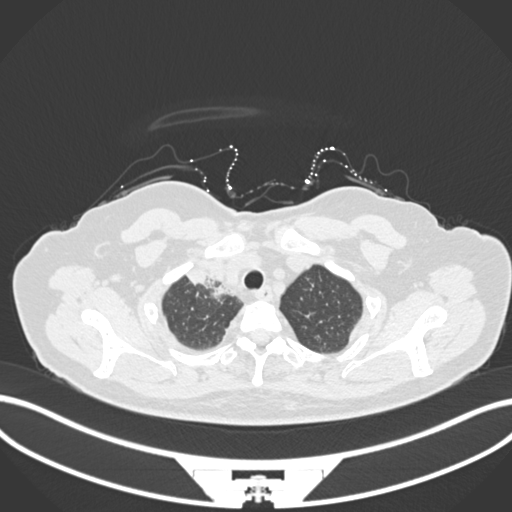
Chest CT, one axial slice; position 148 of 172 along the scan axis; reconstruction kernel B30f; 120 kVp; lung window (W 1500 / L -600 HU); 1 mm slice thickness; 512 × 512 image matrix, field of view 400 × 400 mm. Female patient, age 52 years. Case-level facts recorded for this patient, not image findings: clinical TNM (as recorded): T3 N1 M1.
Outlined on this slice (bounding box drawn by a radiologist):
- lung tumour (recorded histology: adenocarcinoma): bounding box (x1, y1, x2, y2) in pixels: (184, 264, 233, 303)